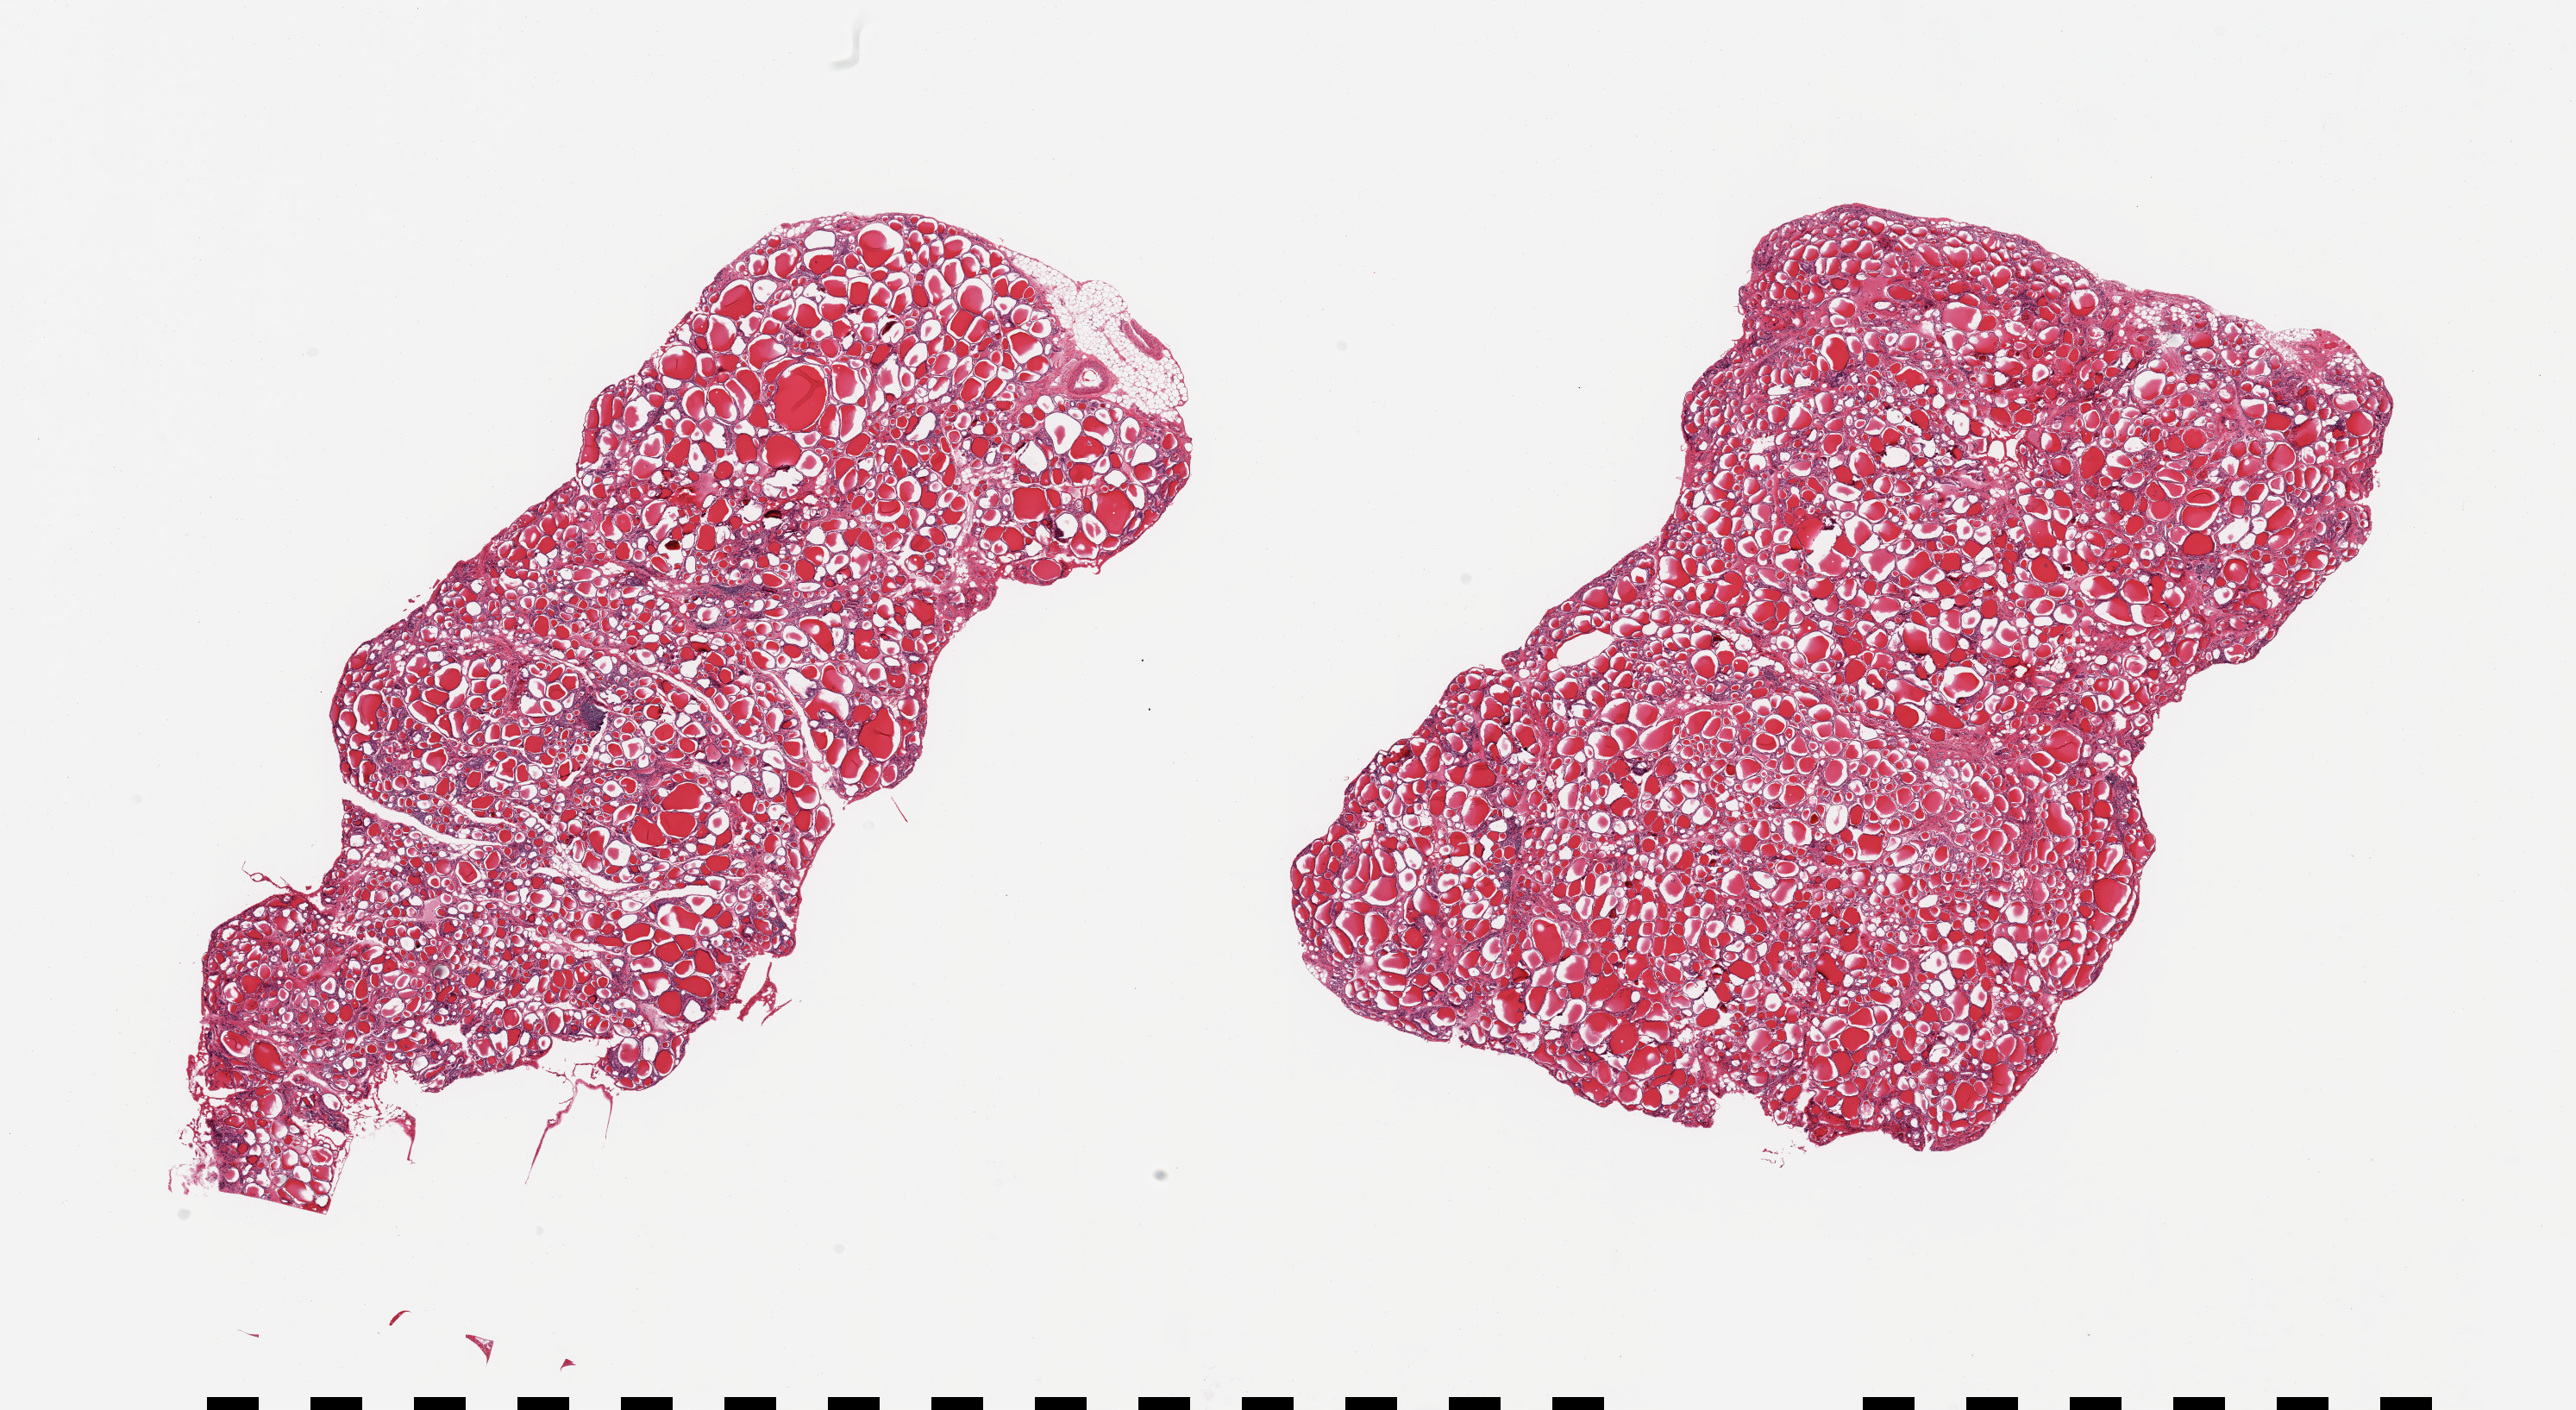
Hematoxylin and eosin (H&E) whole-slide image — whole scanned area (about 23.6 x 12.9 mm, from a 20x scan) shown as a low-resolution overview; PAXgene-fixed paraffin-embedded (PFPE) section; sampled site (target tissue): thyroid; tissue donor sample.
• review note (as recorded): 2 pieces; two small collections of lymphocytes